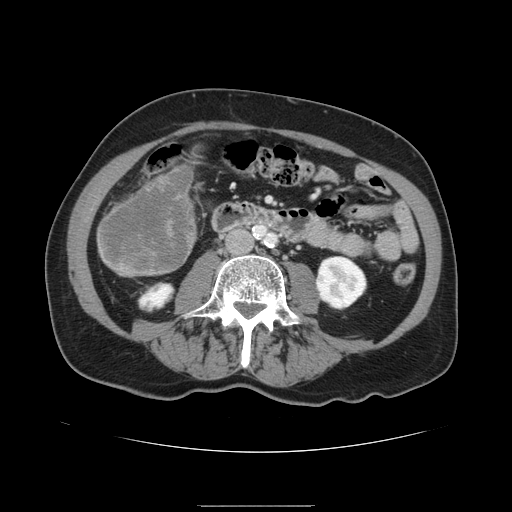
Contrast-enhanced abdominal CT, one axial slice. Slice 28 of 168 in the series (ordered by position). 120 kVp. Intravenous contrast given. Soft-tissue window (W 400 / L 40 HU). 2.5 mm slice thickness. 512 × 512 image matrix. Male patient, age 74 years. From the clinical record (not read from this slice): diagnosis: colorectal cancer liver metastases, imaged before liver resection; multiple liver metastases: no; largest metastasis: 14.5 cm; disease in both lobes: yes.
Outlined on this slice (outlined manually by an expert reader):
- liver: bounding box <96,163,197,277> (left, top, right, bottom; pixels)
- liver metastasis: <100,171,193,273>